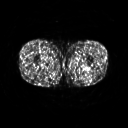
FDG PET of an extremity soft-tissue mass (from a PET/CT study), one axial slice; slice 233 of 267 in the series (ordered by position); 3.27 mm slice thickness; 128 × 128 image matrix, field of view 500 × 500 mm. Male patient, age 27 years. From the clinical record (not read from this slice): histological type: extraskeletal osteosarcoma; grade: high; site of the primary tumour: left adductur.
Outlined on this slice (expert contour drawn on MRI and transferred to this co-registered scan by the dataset authors):
- gross tumour volume (mass): bounding box <68,60,94,74> (left, top, right, bottom; pixels)